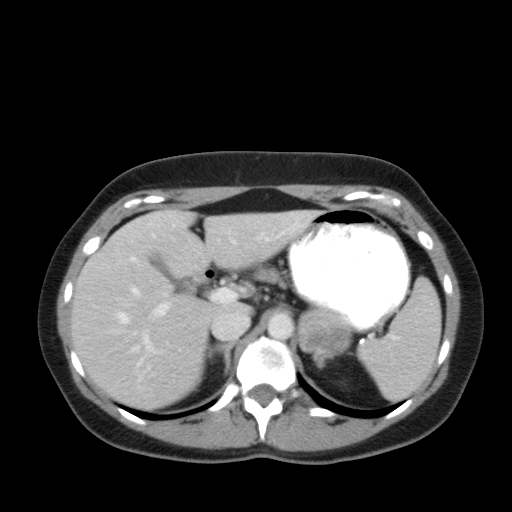
Contrast-enhanced abdominal CT, one axial slice. Slice 36 of 92 in the series (ordered by position). 120 kVp. Intravenous contrast given. Soft-tissue window (W 400 / L 40 HU). 5 mm slice thickness. 512 × 512 image matrix, field of view 369 × 369 mm. Female patient, age 35 years. Case-level facts recorded for this patient, not image findings: diagnosis: adrenocortical carcinoma; tumour side: left adrenal; tumour size at pathology: 6.6 cm; Ki-67 index: 5 %; stage (as recorded): 2.
Structures marked on this image (semi-automatic segmentation, software-assisted and operator-edited):
- mass: bounding box [x1, y1, x2, y2] px = [300, 311, 350, 352]